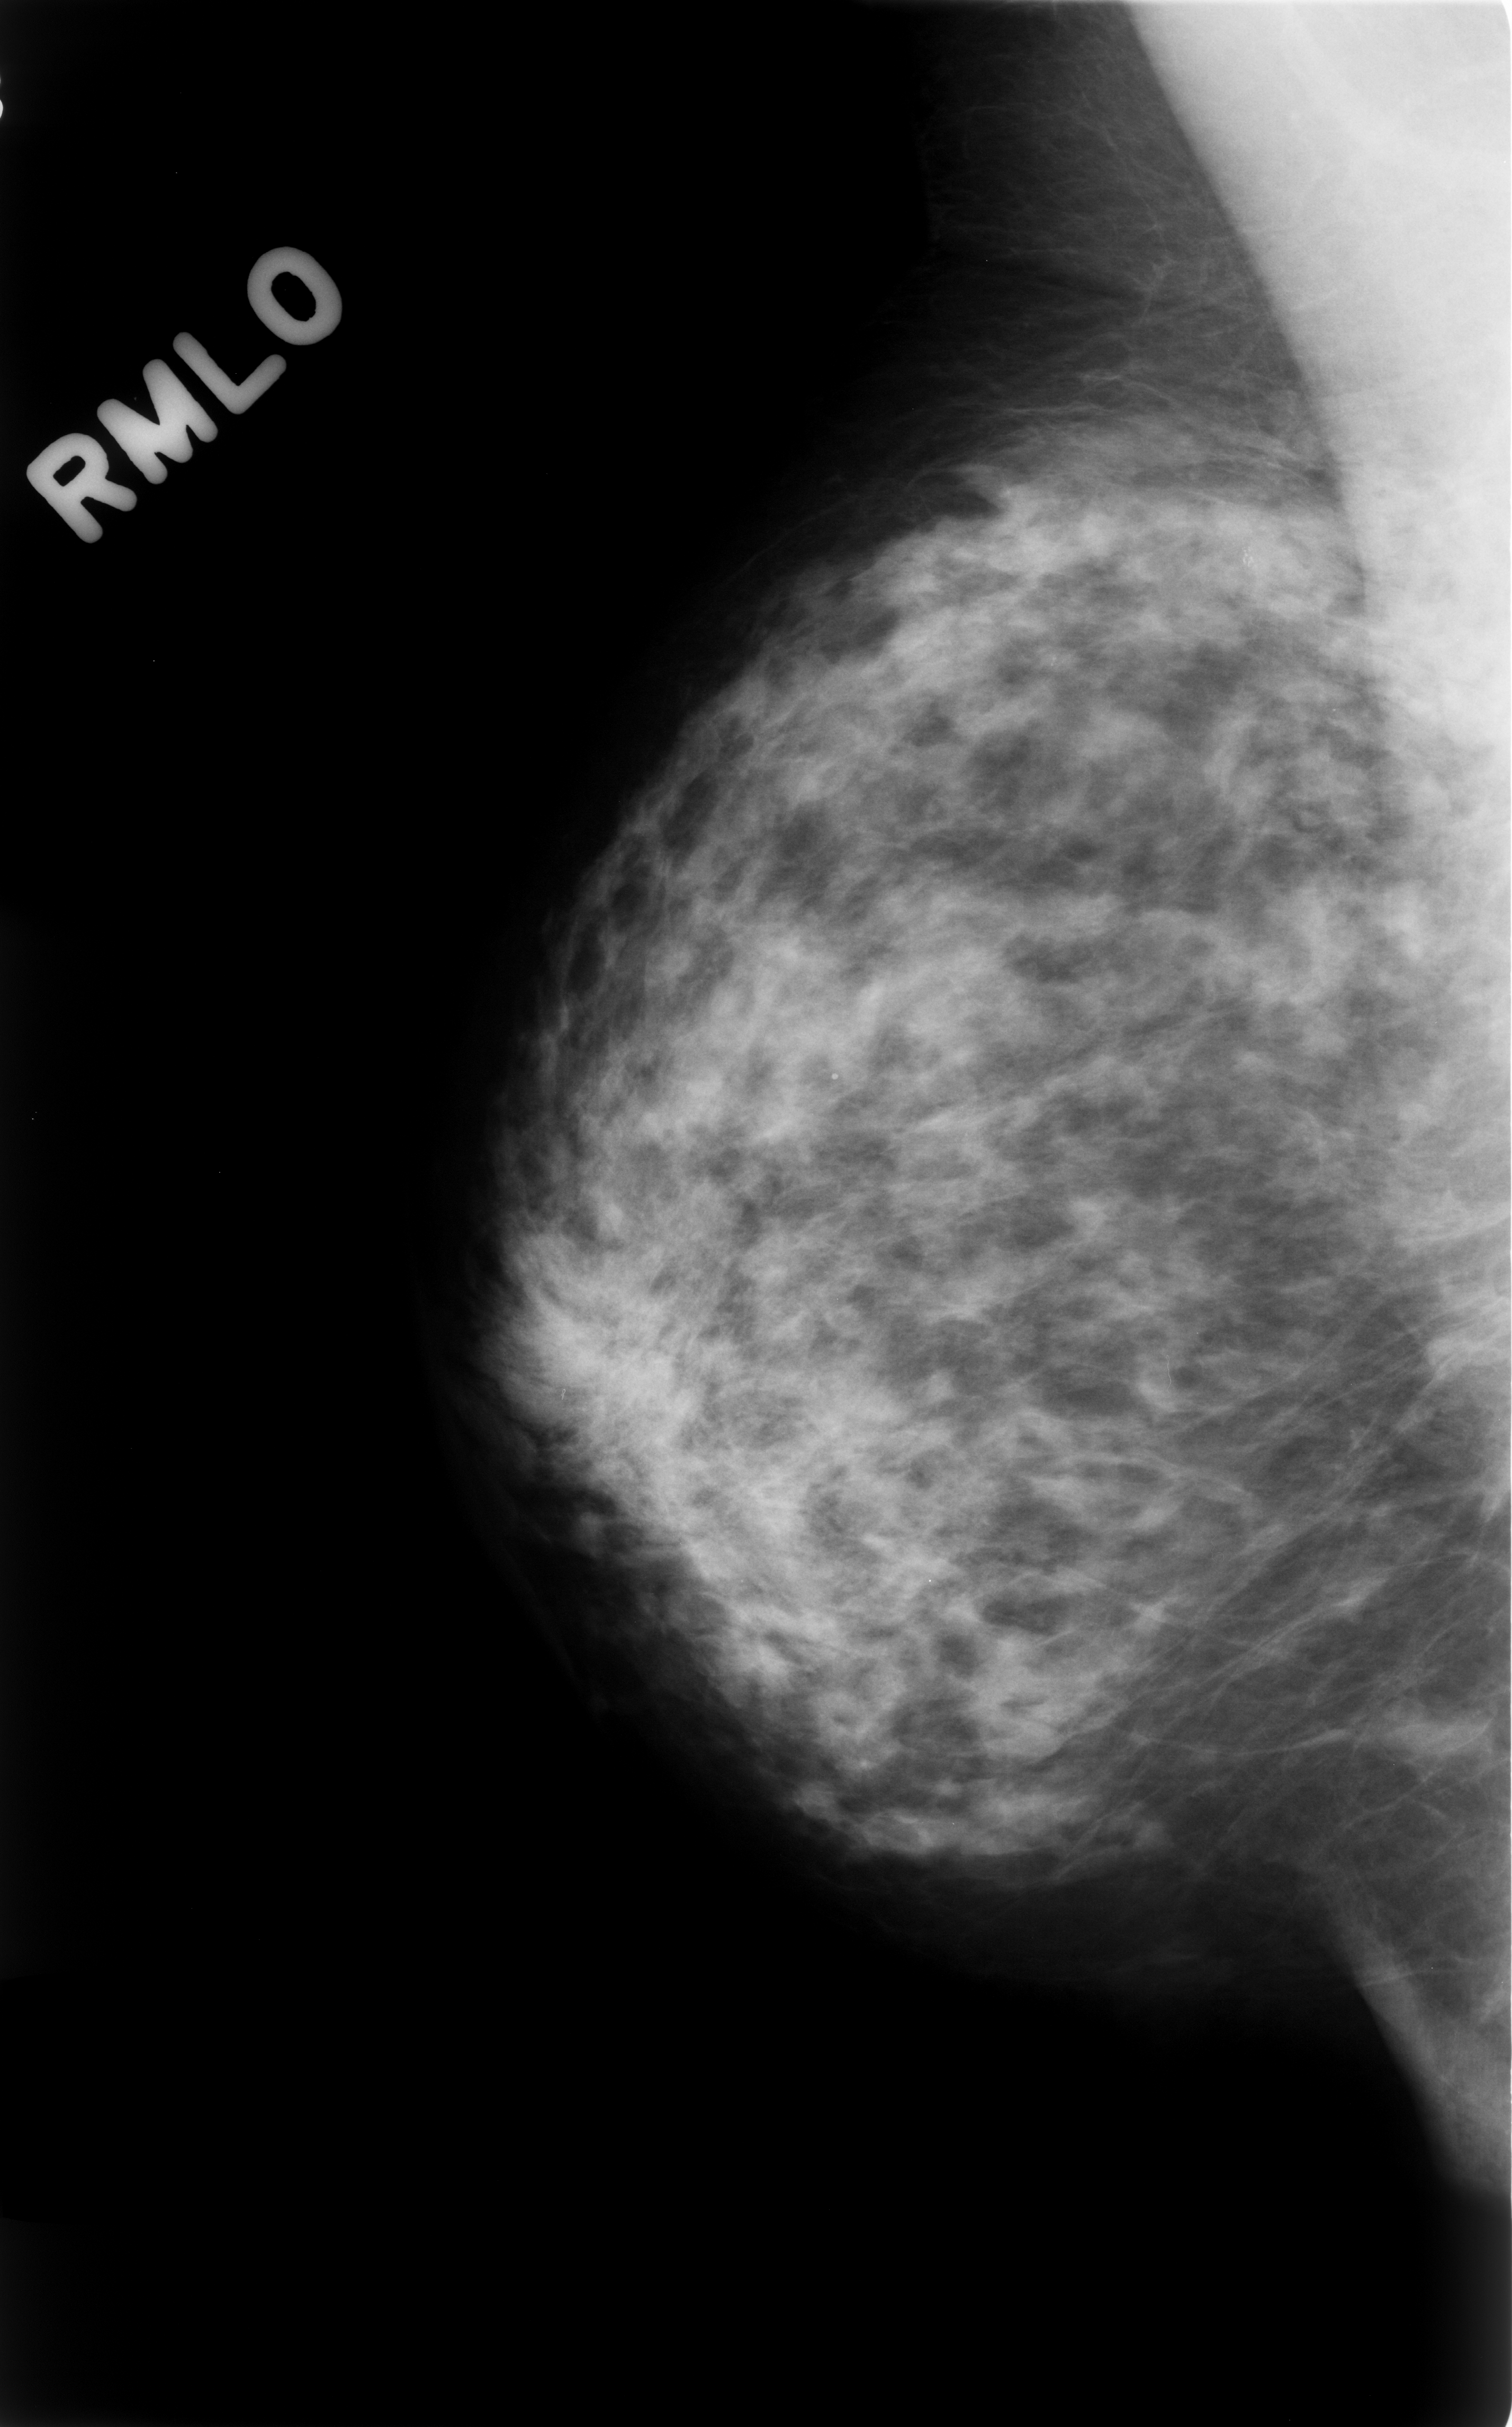
Scanned film-screen mammogram. Right breast. Mediolateral oblique (MLO) view. BI-RADS breast density category 2 (scale 1–4). 1512 × 2427 image matrix.
Expert-marked regions of interest on this image (one box per marked abnormality):
- calcifications, morphology amorphous, distribution clustered; BI-RADS assessment category 4; pathology result (as recorded, not read from the image): benign: bounding box [x1, y1, x2, y2] px = [1143, 461, 1386, 691]